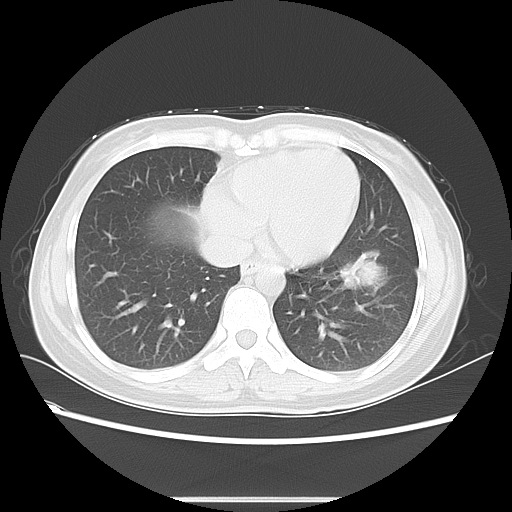
Chest CT, one axial slice; slice 21 of 55 in the series (ordered by position); reconstruction kernel LUNG; lung window (W 1500 / L -600 HU); 5 mm slice thickness; 512 × 512 image matrix. Female patient, age 41 years. Case-level facts recorded for this patient, not image findings: clinical TNM (as recorded): T1c N3 M1b.
Outlined on this slice (rectangle marked by the reading radiologist):
- lung tumour (recorded histology: adenocarcinoma): bounding box <337,244,387,296> (left, top, right, bottom; pixels)